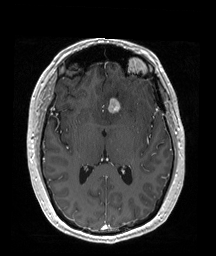
Brain MRI from a brain-tumour surgery series, one axial slice. Slice 96 of 192 in the series (ordered by position). T1-weighted post-contrast. 1 mm slice thickness. 216 × 256 image matrix, field of view 211 × 250 mm. Case-level facts recorded for this patient, not image findings: histopathology: Oligodendroglioma; WHO grade: 2; IDH mutation: yes; tumour location: Left Frontal (septal).
Annotated regions visible in this slice (expert manual segmentation):
- tumour: bounding box [x1, y1, x2, y2] px = [115, 97, 128, 113]